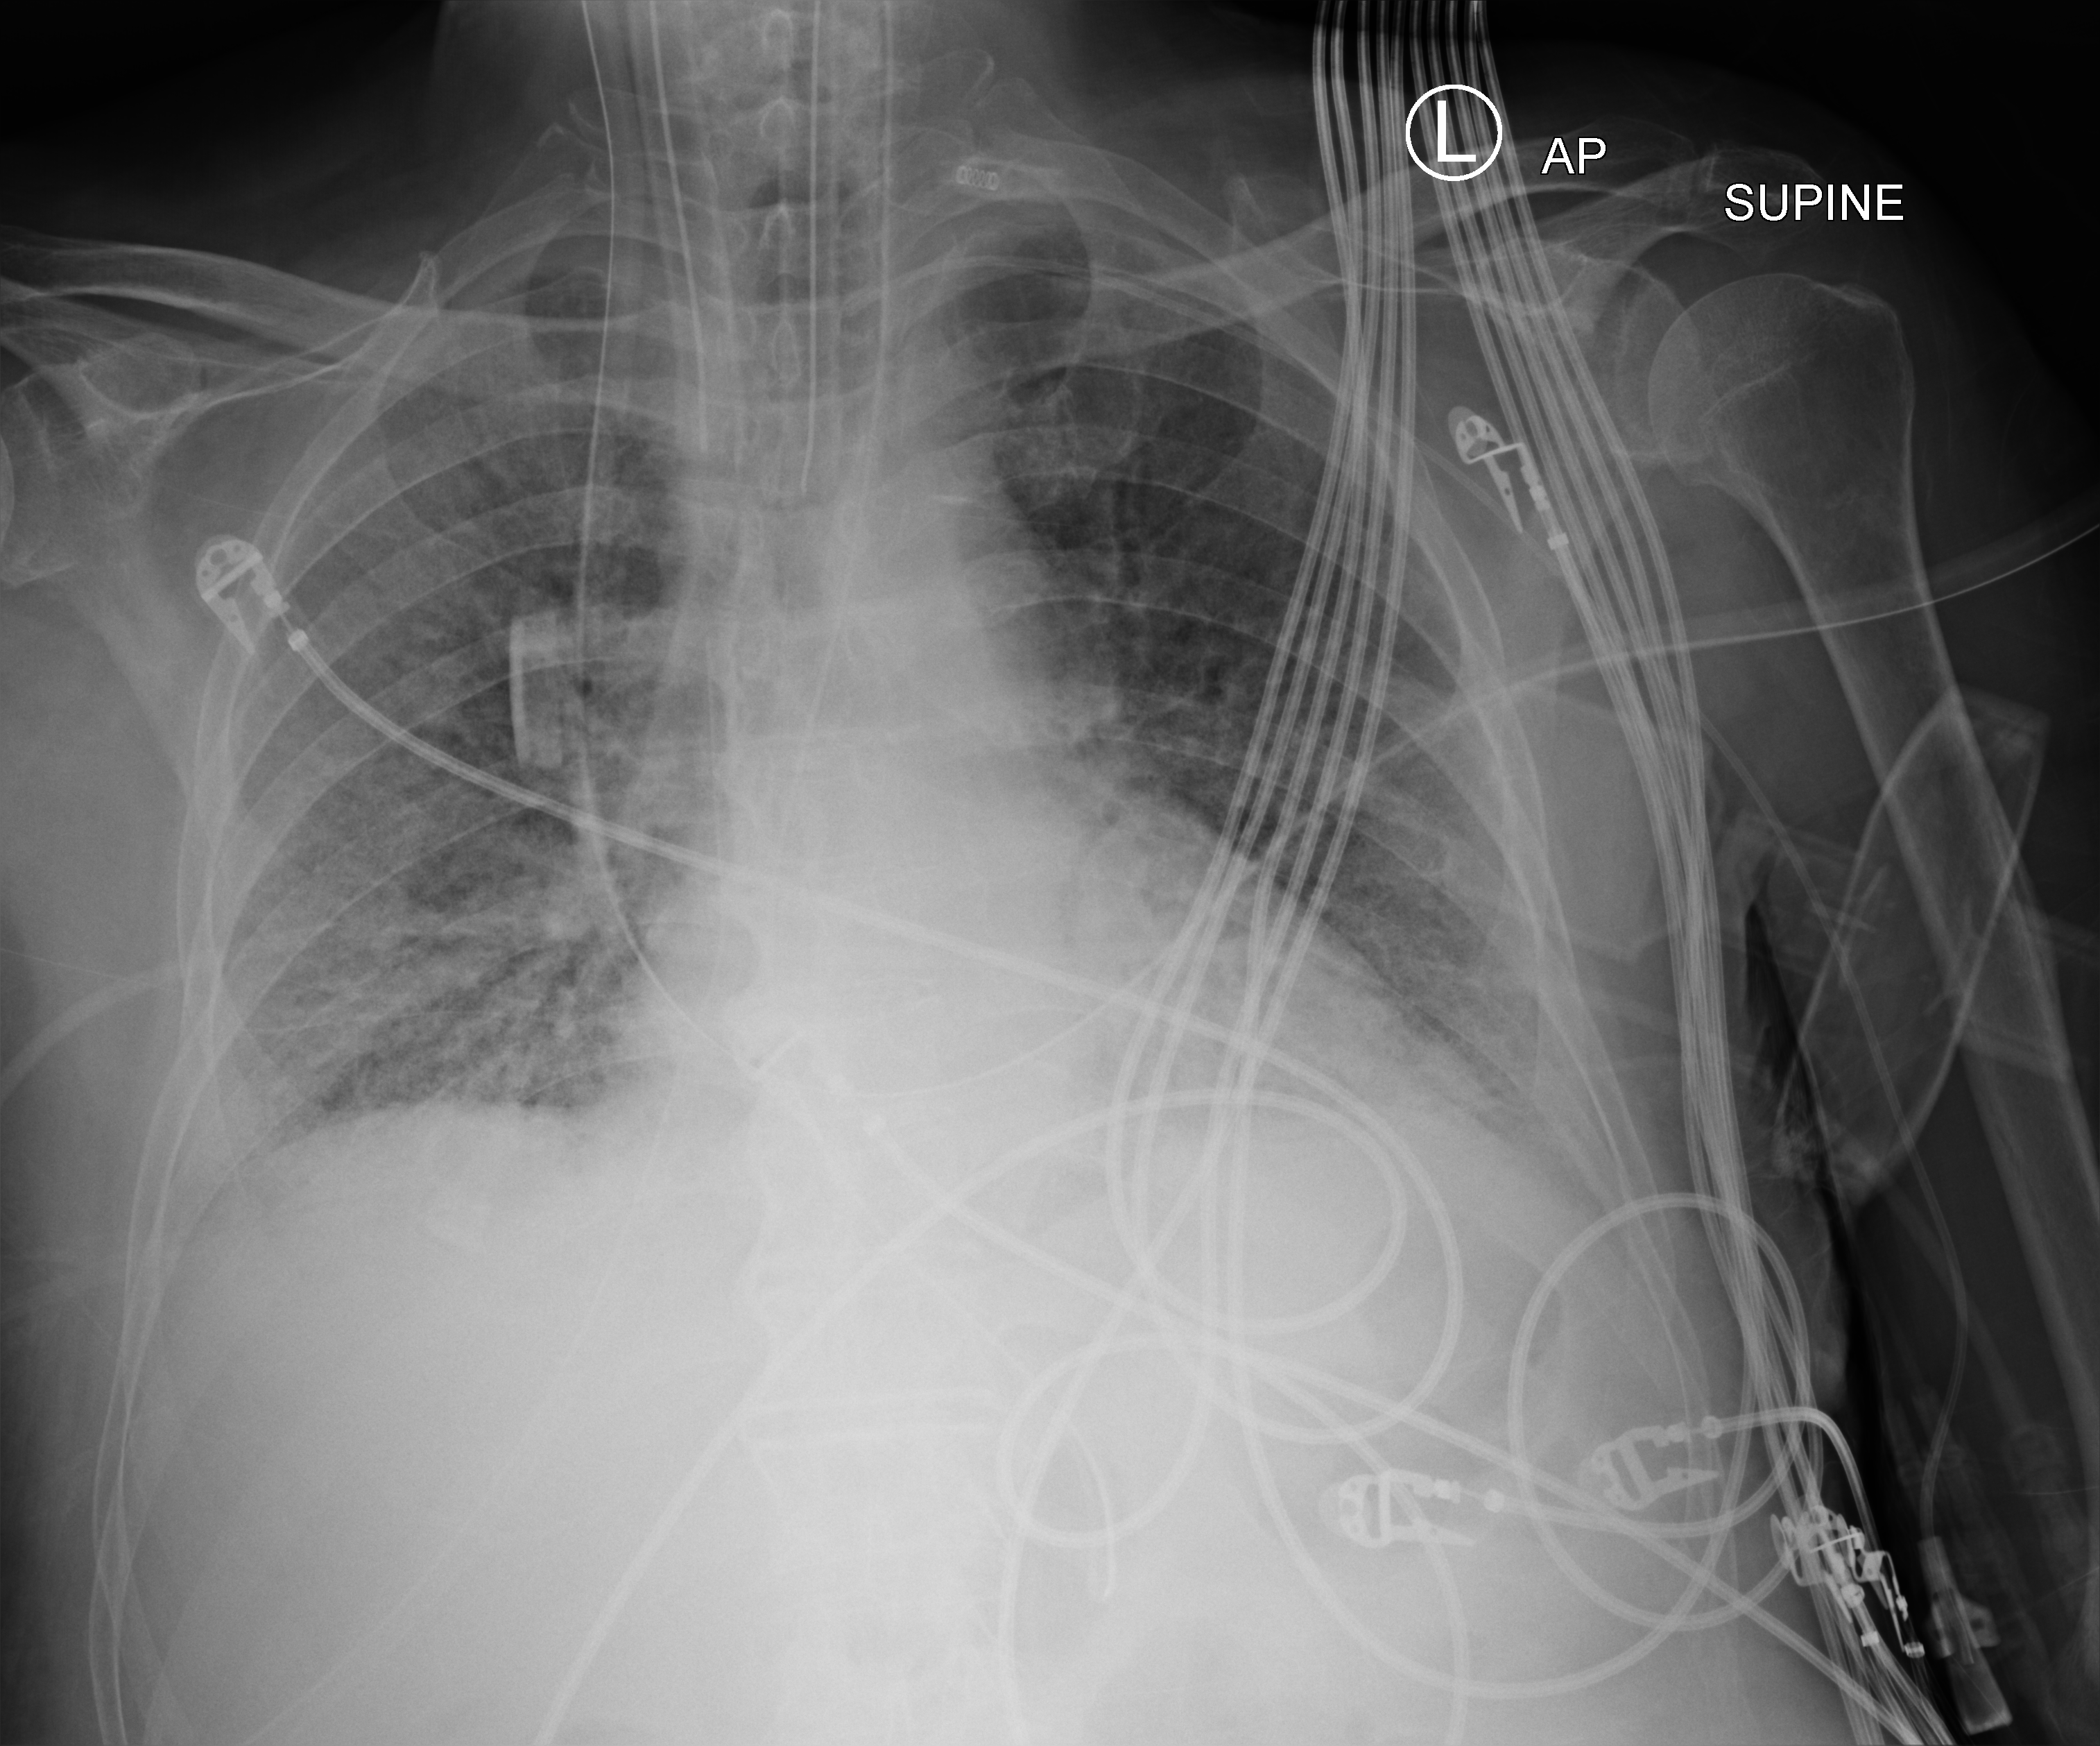
Bedside chest radiograph (computed radiography); anteroposterior (AP) projection. Patient hospitalised with COVID-19; male, aged 75–90 years.
Hospital-stay facts (about this admission, not read from this image; timing relative to this image not recorded): COPD (admission record): no; chronic kidney disease (admission record): no.